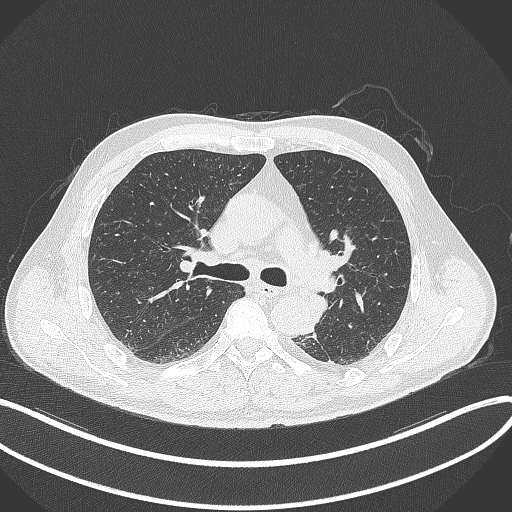
Chest CT, one axial slice. Slice 220 of 329 in the series (ordered by position). 120 kVp. Lung window (W 1500 / L -600 HU). 1 mm slice thickness. 512 × 512 image matrix, field of view 400 × 400 mm. Patient: male, 59 years. Case-level facts recorded for this patient, not image findings: clinical TNM (as recorded): T2a N2 M0.
Structures marked on this image (bounding box drawn by a radiologist):
- lung tumour (recorded histology: squamous cell carcinoma): bounding box <303,295,330,326> (left, top, right, bottom; pixels)